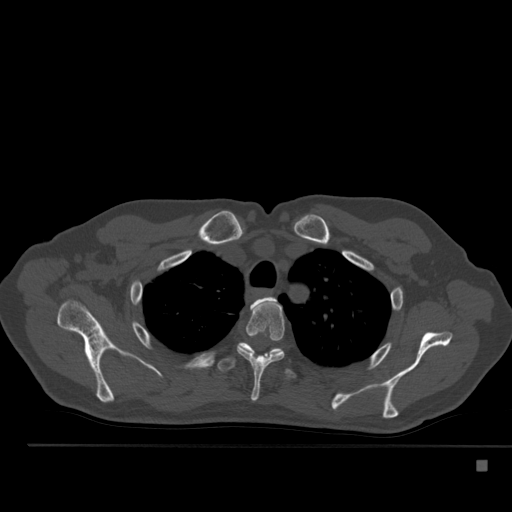
CT including the spine, one axial slice. Position 394 of 517 along the scan axis. Reconstruction kernel Br40s. 120 kVp. Bone window (W 1800 / L 400 HU). 1.5 mm slice thickness. 512 × 512 image matrix, field of view 408 × 408 mm. Male patient, age 70 years. Case-level facts recorded for this patient, not image findings: primary cancer: renal.
Annotated regions visible in this slice (semi-automatic segmentation, software-assisted and operator-edited):
- T2 vertebra: bounding box <253,297,276,307> (left, top, right, bottom; pixels)
- T3 vertebra: <237,301,285,401>
- T4 vertebra: <217,342,297,379>